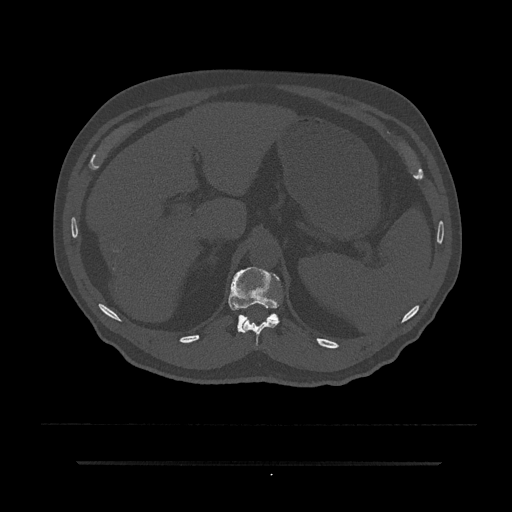
CT including the spine, one axial slice; slice 239 of 797 in the series (ordered by position); reconstruction kernel Br40s/3; 120 kVp; bone window (W 1800 / L 400 HU); 0.5 mm slice thickness; 512 × 512 image matrix, field of view 464 × 464 mm. Patient: male, 59 years. From the clinical record (not read from this slice): primary cancer: bile ducts.
Structures marked on this image (semi-automatic segmentation, software-assisted and operator-edited):
- T11 vertebra: bounding box [x1, y1, x2, y2] px = [242, 319, 279, 346]
- T12 vertebra: [229, 267, 280, 333]